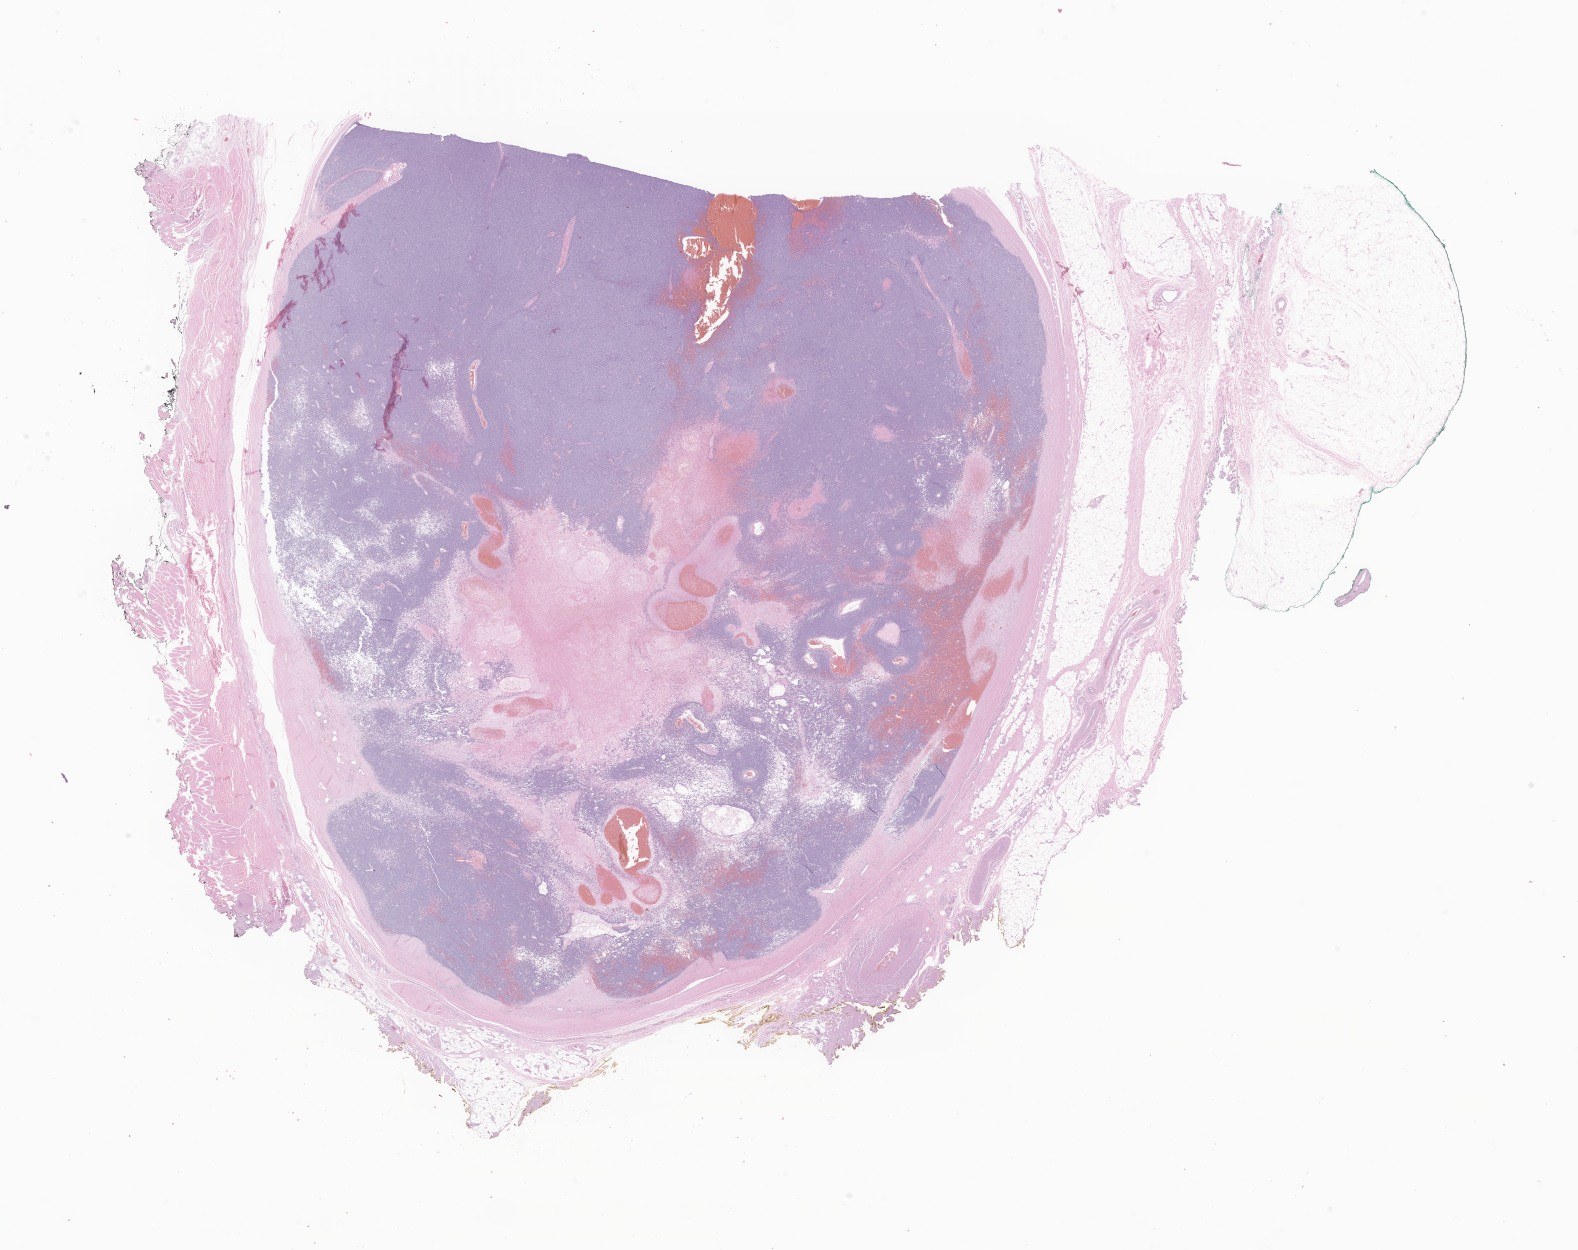
Digitized haematoxylin and eosin-stained section of tumor tissue from the soft tissue of lower extremity, a low-resolution overview of the entire scanned area, about 26.6 x 21.1 mm. Patient: male, age 195 months.
Specimen: formalin-fixed, paraffin-embedded (FFPE) tissue.